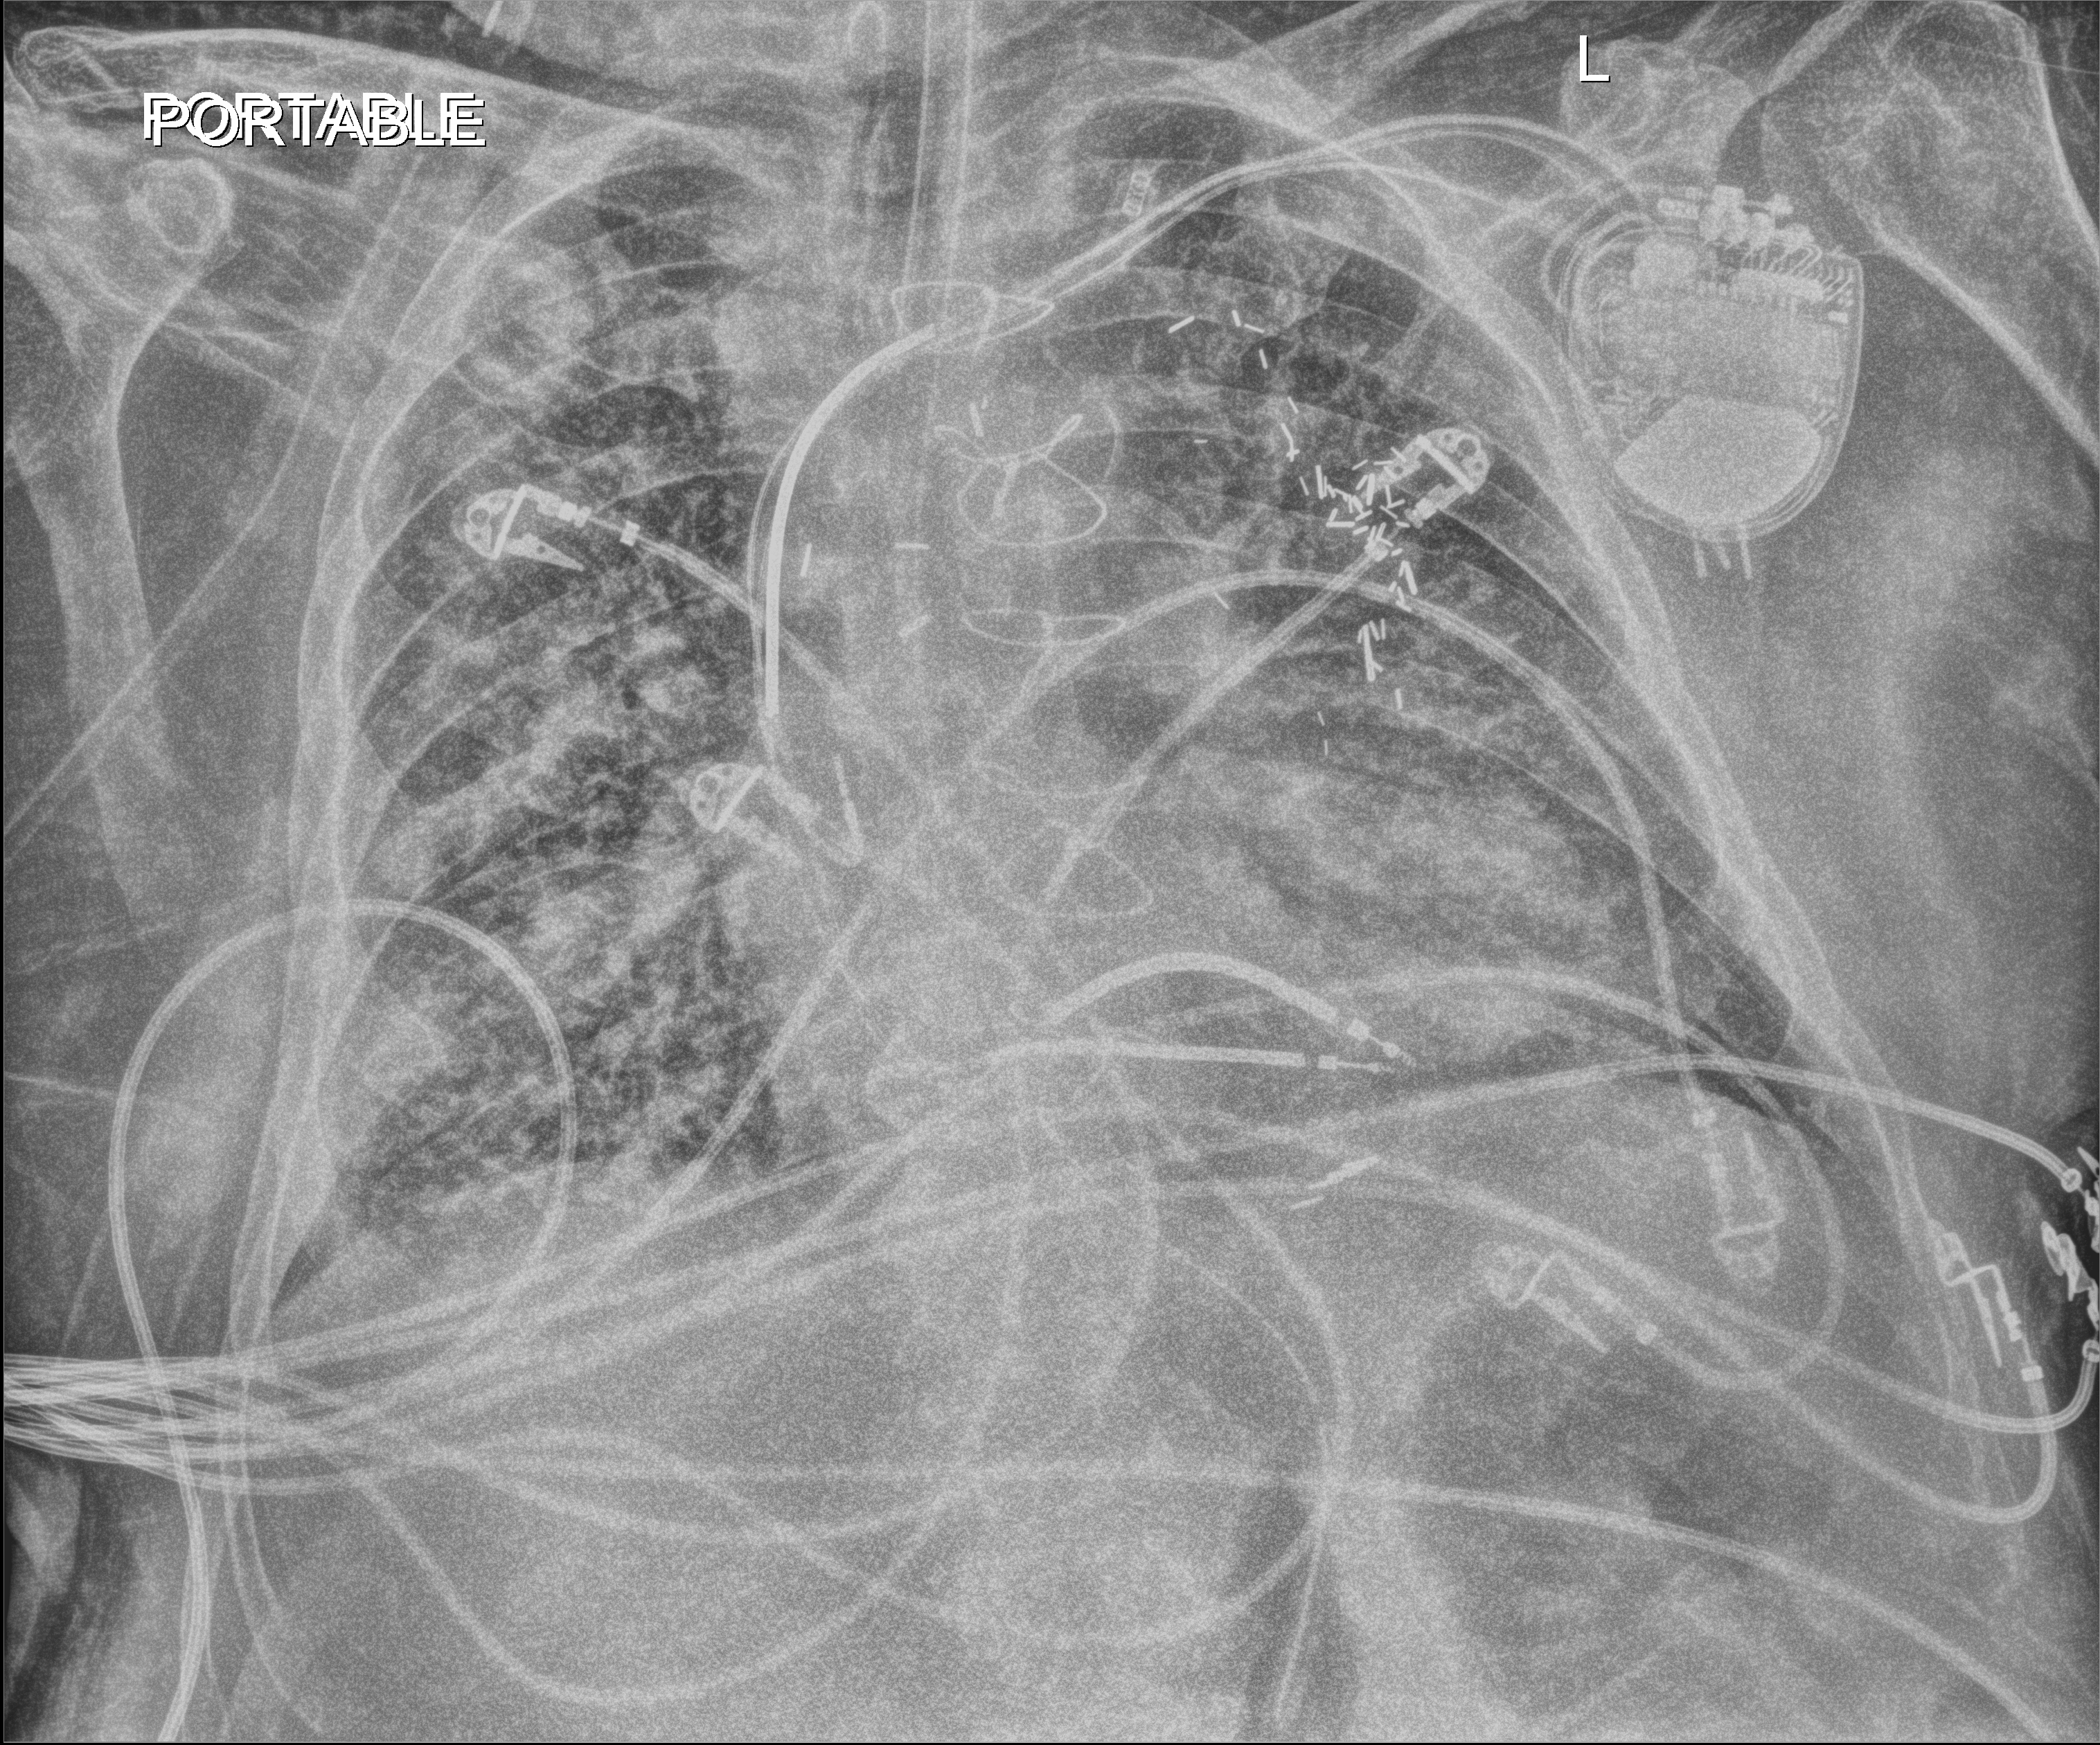
Bedside chest radiograph (digital radiography), anteroposterior (AP) projection. Patient hospitalised with COVID-19; male, aged 60–74 years.
Admission-level facts for this patient (not findings on this image; timing relative to this image not recorded): mechanically ventilated during this hospital stay: yes.